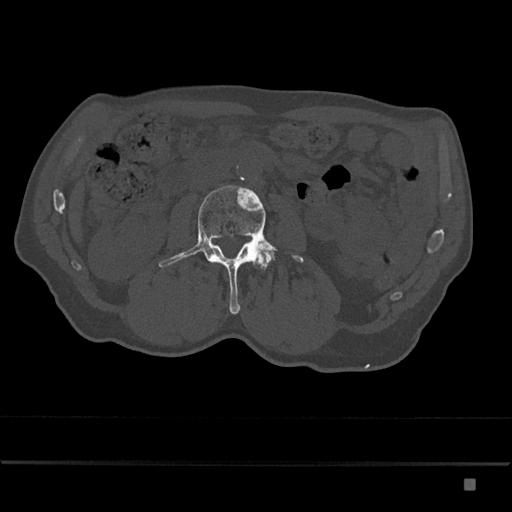
CT including the spine, one axial slice; position 407 of 797 along the scan axis; reconstruction kernel Br40s/3; bone window (W 1800 / L 400 HU); 0.5 mm slice thickness; 512 × 512 image matrix, field of view 390 × 390 mm. Patient: male, 72 years. Case-level facts recorded for this patient, not image findings: primary cancer: prostate.
Structures marked on this image (semi-automatically segmented with operator editing):
- L3 vertebra: bounding box <158,185,304,314> (left, top, right, bottom; pixels)
- L4 vertebra: <259,251,273,269>